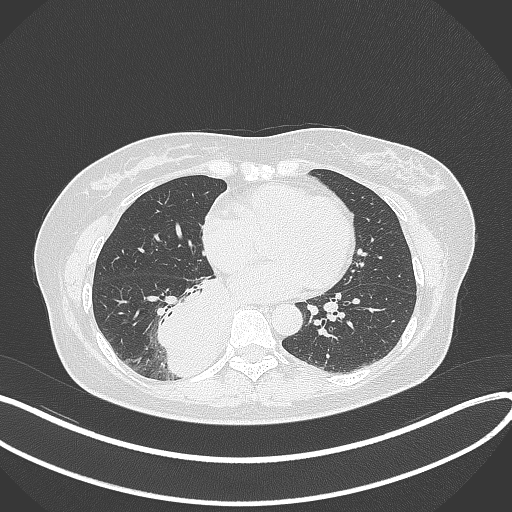
Chest CT, one axial slice. Slice 144 of 331 in the series (ordered by position). Lung window (W 1500 / L -600 HU). 1 mm slice thickness. 512 × 512 image matrix, field of view 400 × 400 mm. Patient: female, 54 years. Case-level facts recorded for this patient, not image findings: clinical TNM (as recorded): T4 N0 M0.
Outlined on this slice (bounding box drawn by a radiologist):
- lung tumour (recorded histology: adenocarcinoma): bounding box [x1, y1, x2, y2] px = [155, 276, 238, 378]